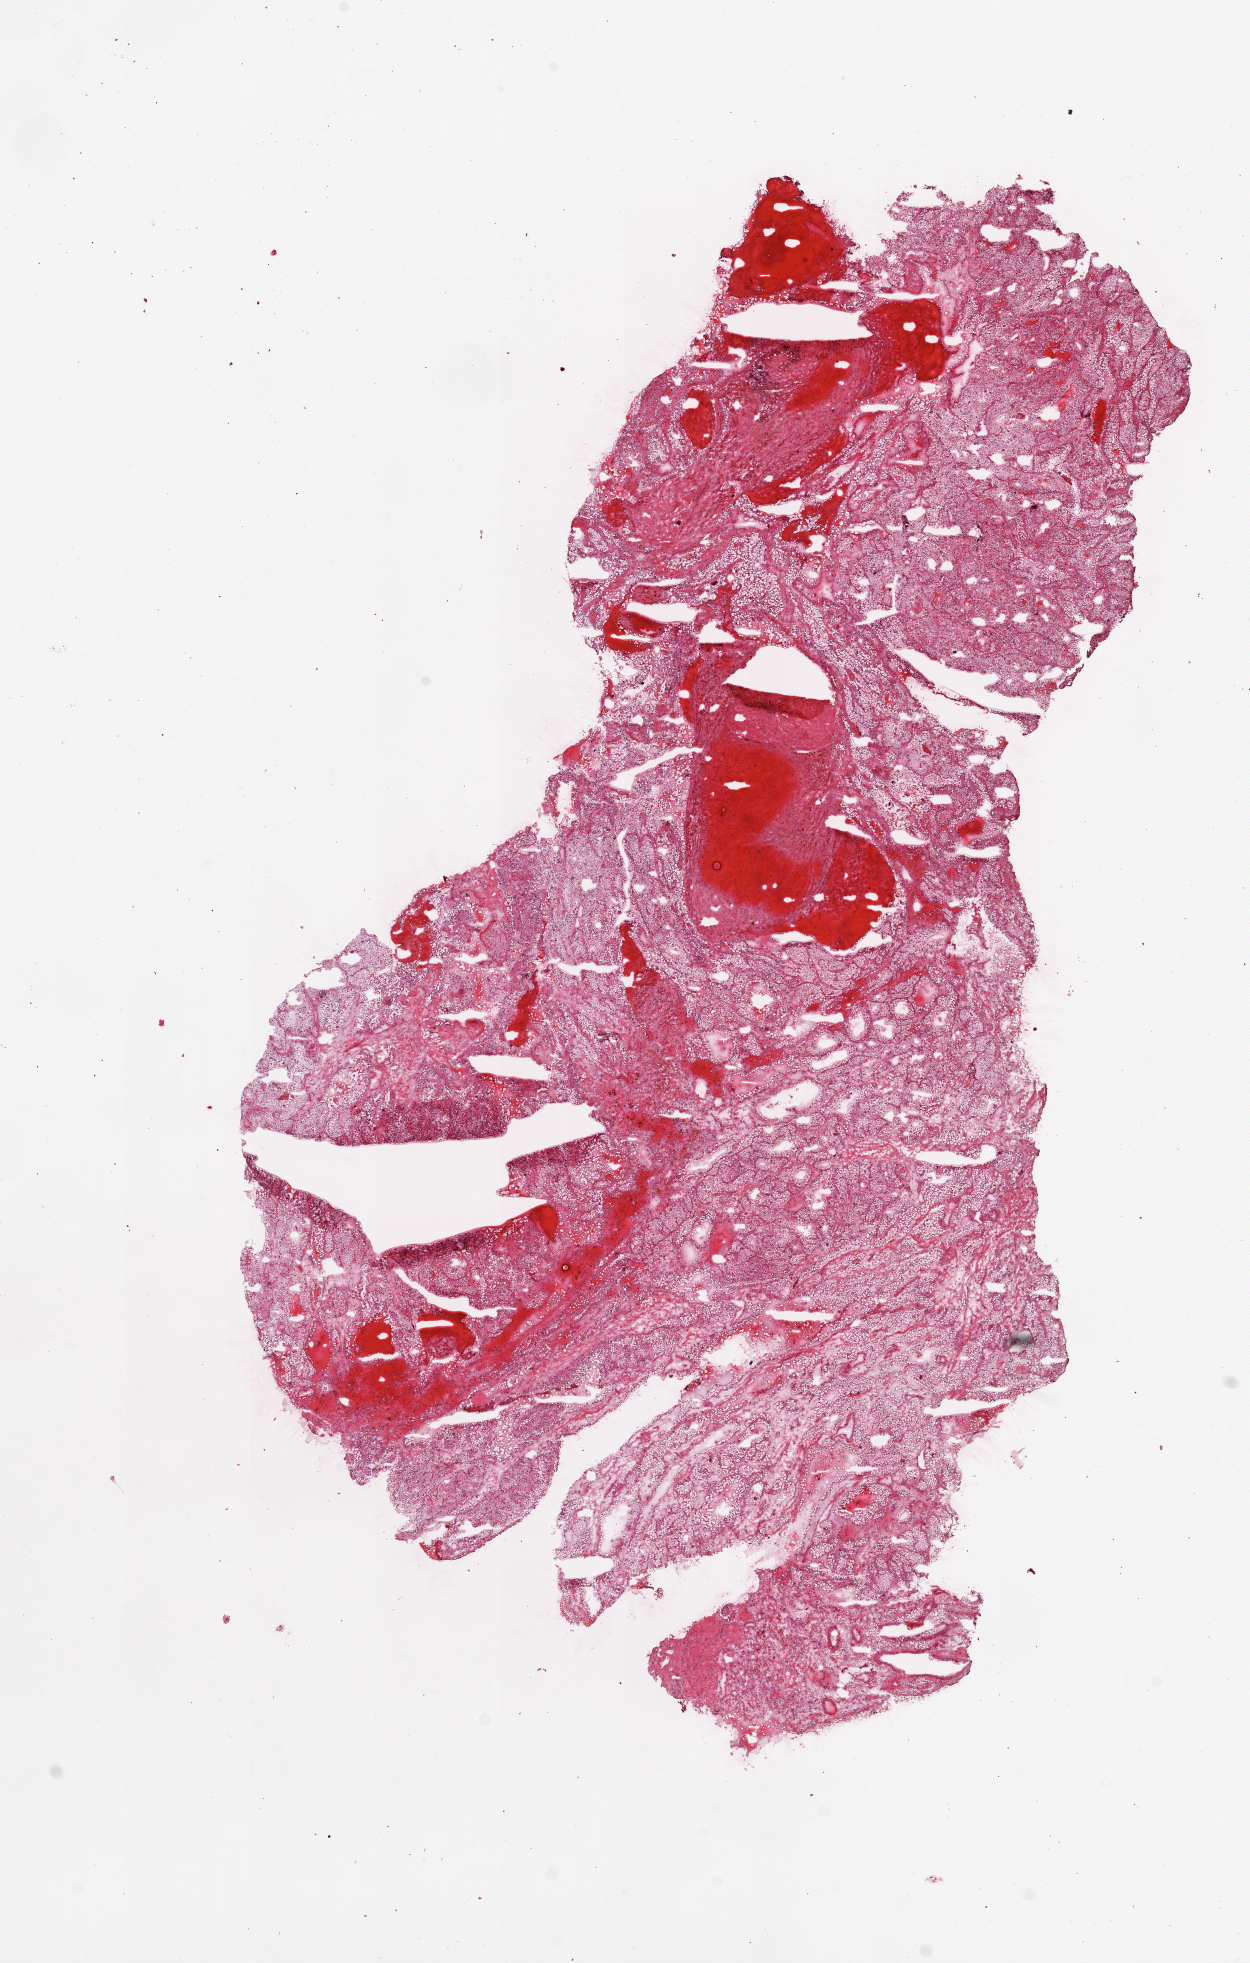
Digitized Hematoxylin and eosin (H&E) stained tissue section (whole slide), shown as a low-resolution overview of the whole scanned area (about 10.0 x 15.8 mm, acquisition: 20x scan); frozen section from the top of the tissue portion; primary tumour sample from the kidney. Patient: male, age at initial diagnosis 42 years. Histologic grade: G3 (poorly differentiated). Composition of this section per pathologist review: tumour cells 85%, tumour nuclei 90%, normal cells 0%, stromal cells 5%, necrosis 10%.
AJCC pathologic stage: I. Laterality: right. TNM: T1a NX M0. Histologic diagnosis: Clear cell adenocarcinoma, NOS.